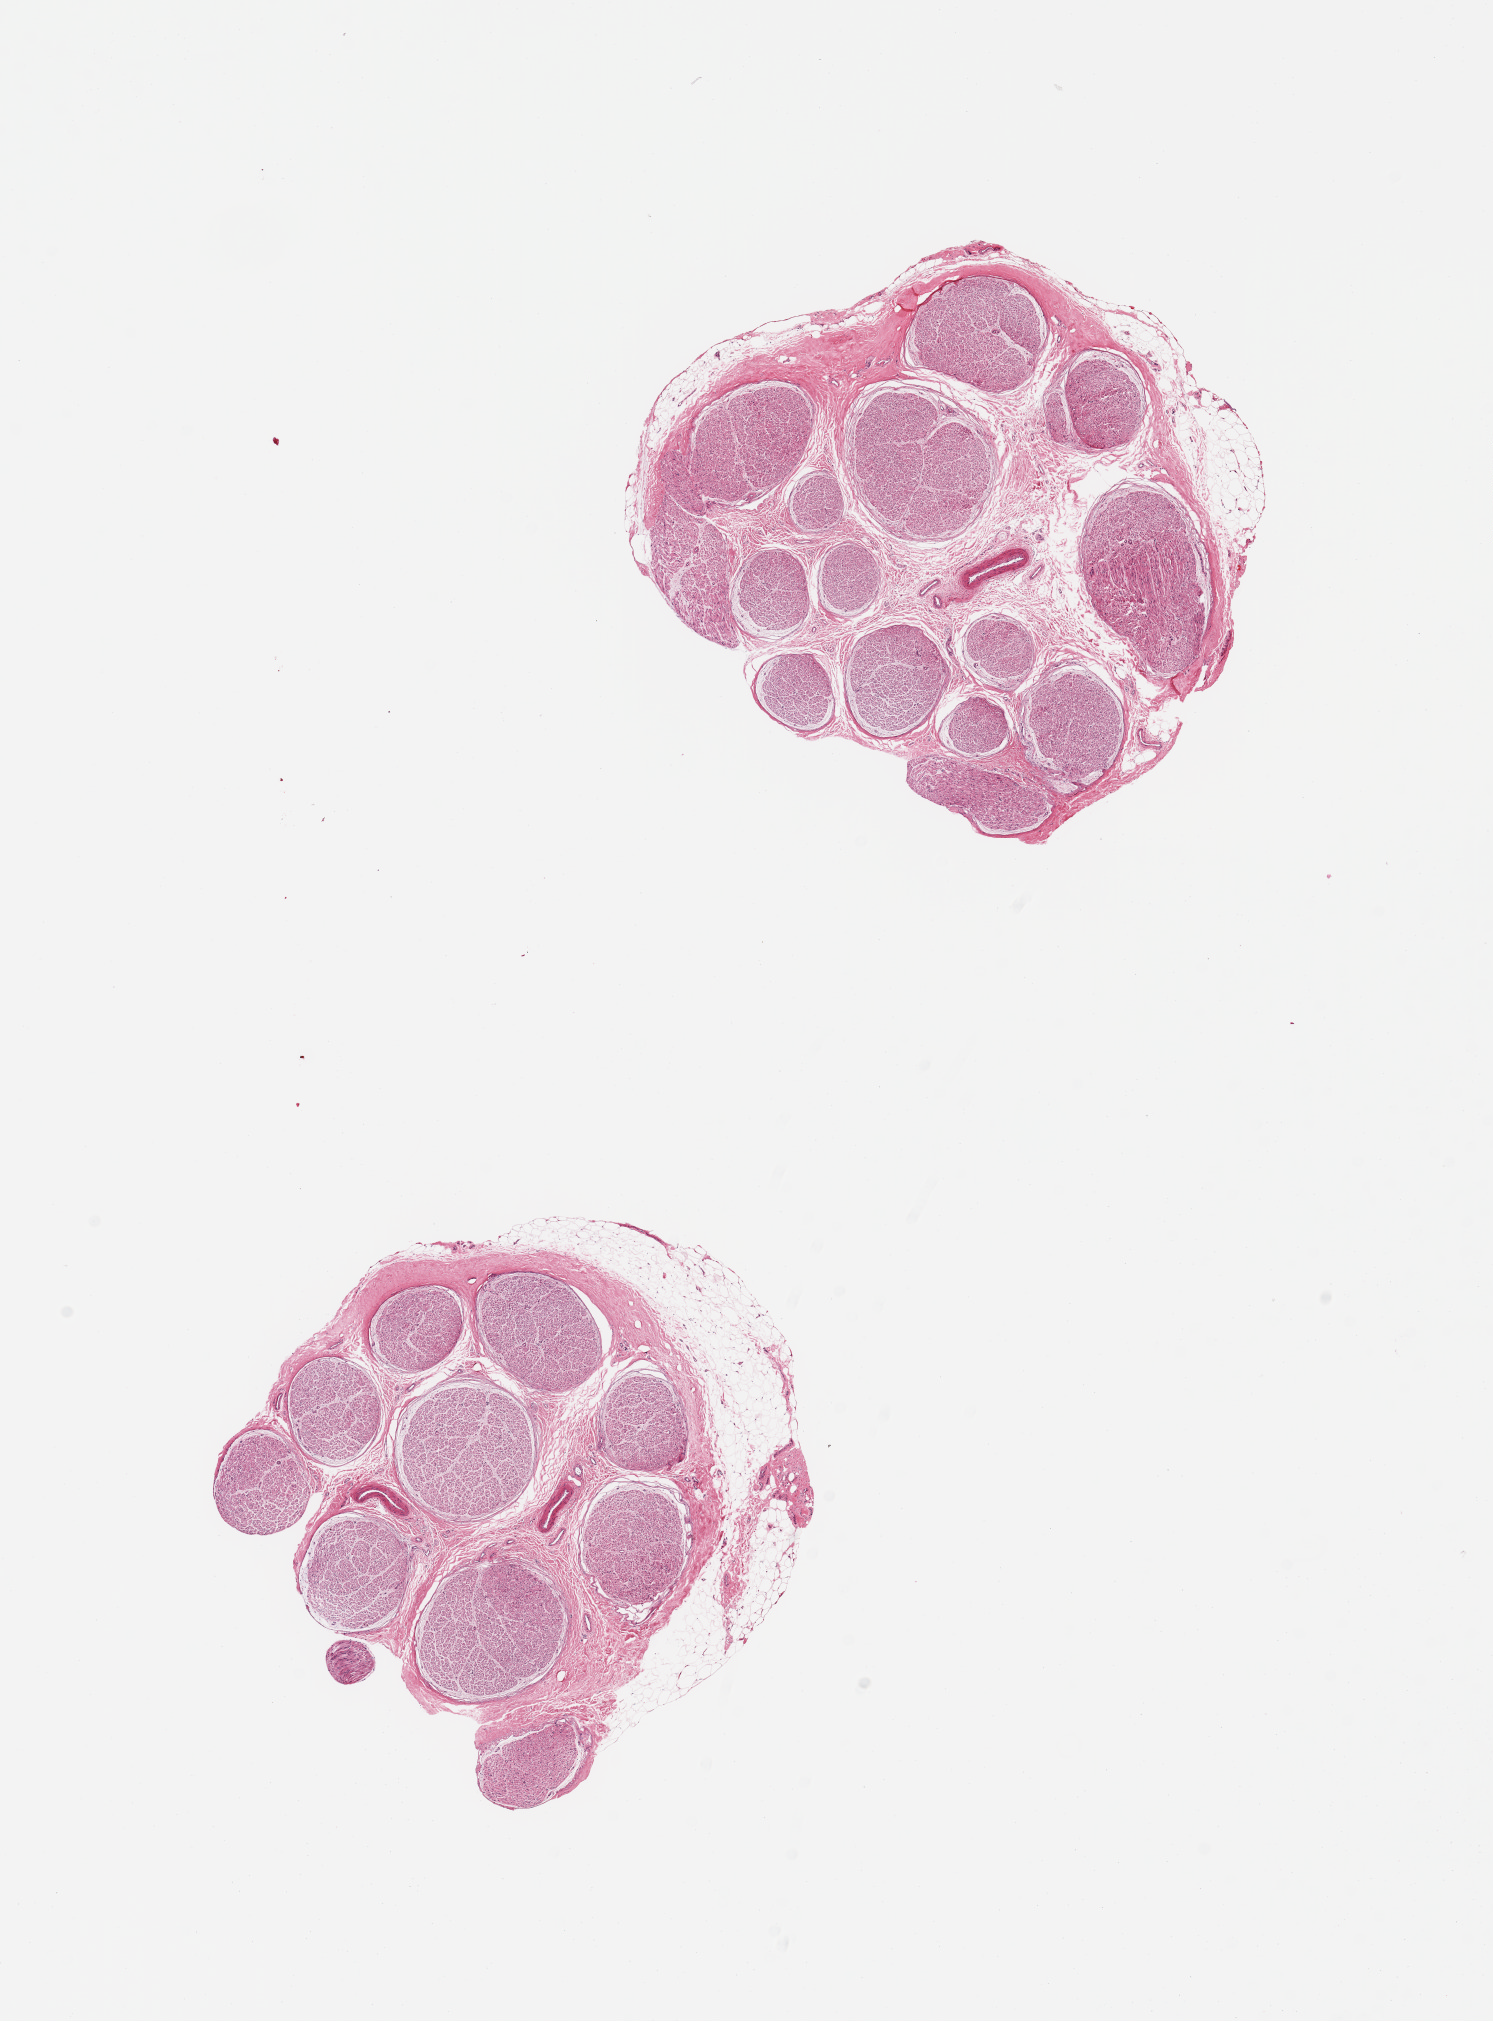
Digitized H&E-stained section — low-resolution overview of the scanned area, about 11.8 x 16.0 mm (acquisition: 20x scan). PAXgene-fixed paraffin-embedded (PFPE) section. Sampled site (target tissue): tibial nerve. Donor tissue sample.
* reviewer comment on this tissue sample: 2 pieces; up to 0.7mm external fat